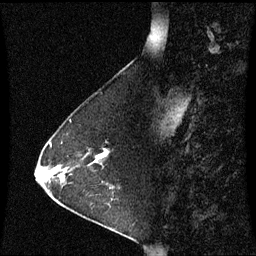
Breast MRI (dynamic contrast-enhanced), one sagittal slice; position 20 of 60 along the scan axis; dynamic contrast-enhanced series, image 2 of 3 at this slice position (ordered by acquisition); 1.5 T; TE 4.2 ms, TR 8.9 ms; 2 mm slice thickness; 256 × 256 image matrix. Patient: female, 63 years. Case-level facts recorded for this patient, not image findings: setting: breast cancer imaged before/during neoadjuvant chemotherapy; receptor status: HR-positive, HER2-negative.
Annotated regions visible in this slice (semi-automatically segmented with operator editing):
- analysis volume of interest (the breast-tissue region the enhancement analysis was run in; not a lesion): box from (x=76, y=143) to (x=111, y=172) px
- tumour enhancement mask (voxels above the 70 % enhancement threshold inside the analysis volume of interest): (x=96, y=153)–(x=106, y=161)